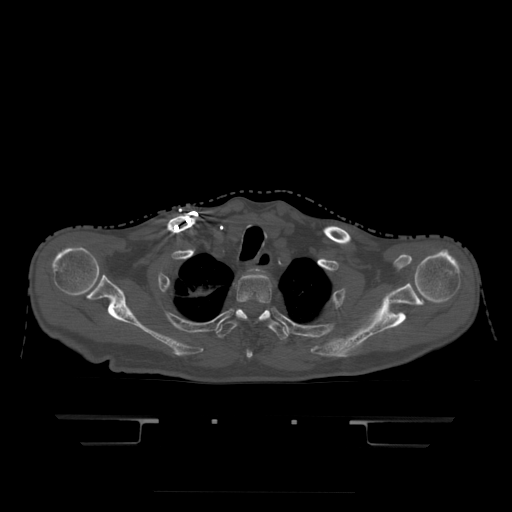
CT including the spine, one axial slice; position 380 of 522 along the scan axis; bone window (W 1800 / L 400 HU); 1.25 mm slice thickness; 512 × 512 image matrix. Patient age 68 years. From the clinical record (not read from this slice): primary cancer: urothelial.
Annotated regions visible in this slice (semi-automatic segmentation, software-assisted and operator-edited):
- T2 vertebra: bounding box (x1, y1, x2, y2) in pixels: (236, 274, 272, 358)
- T3 vertebra: (216, 309, 288, 340)